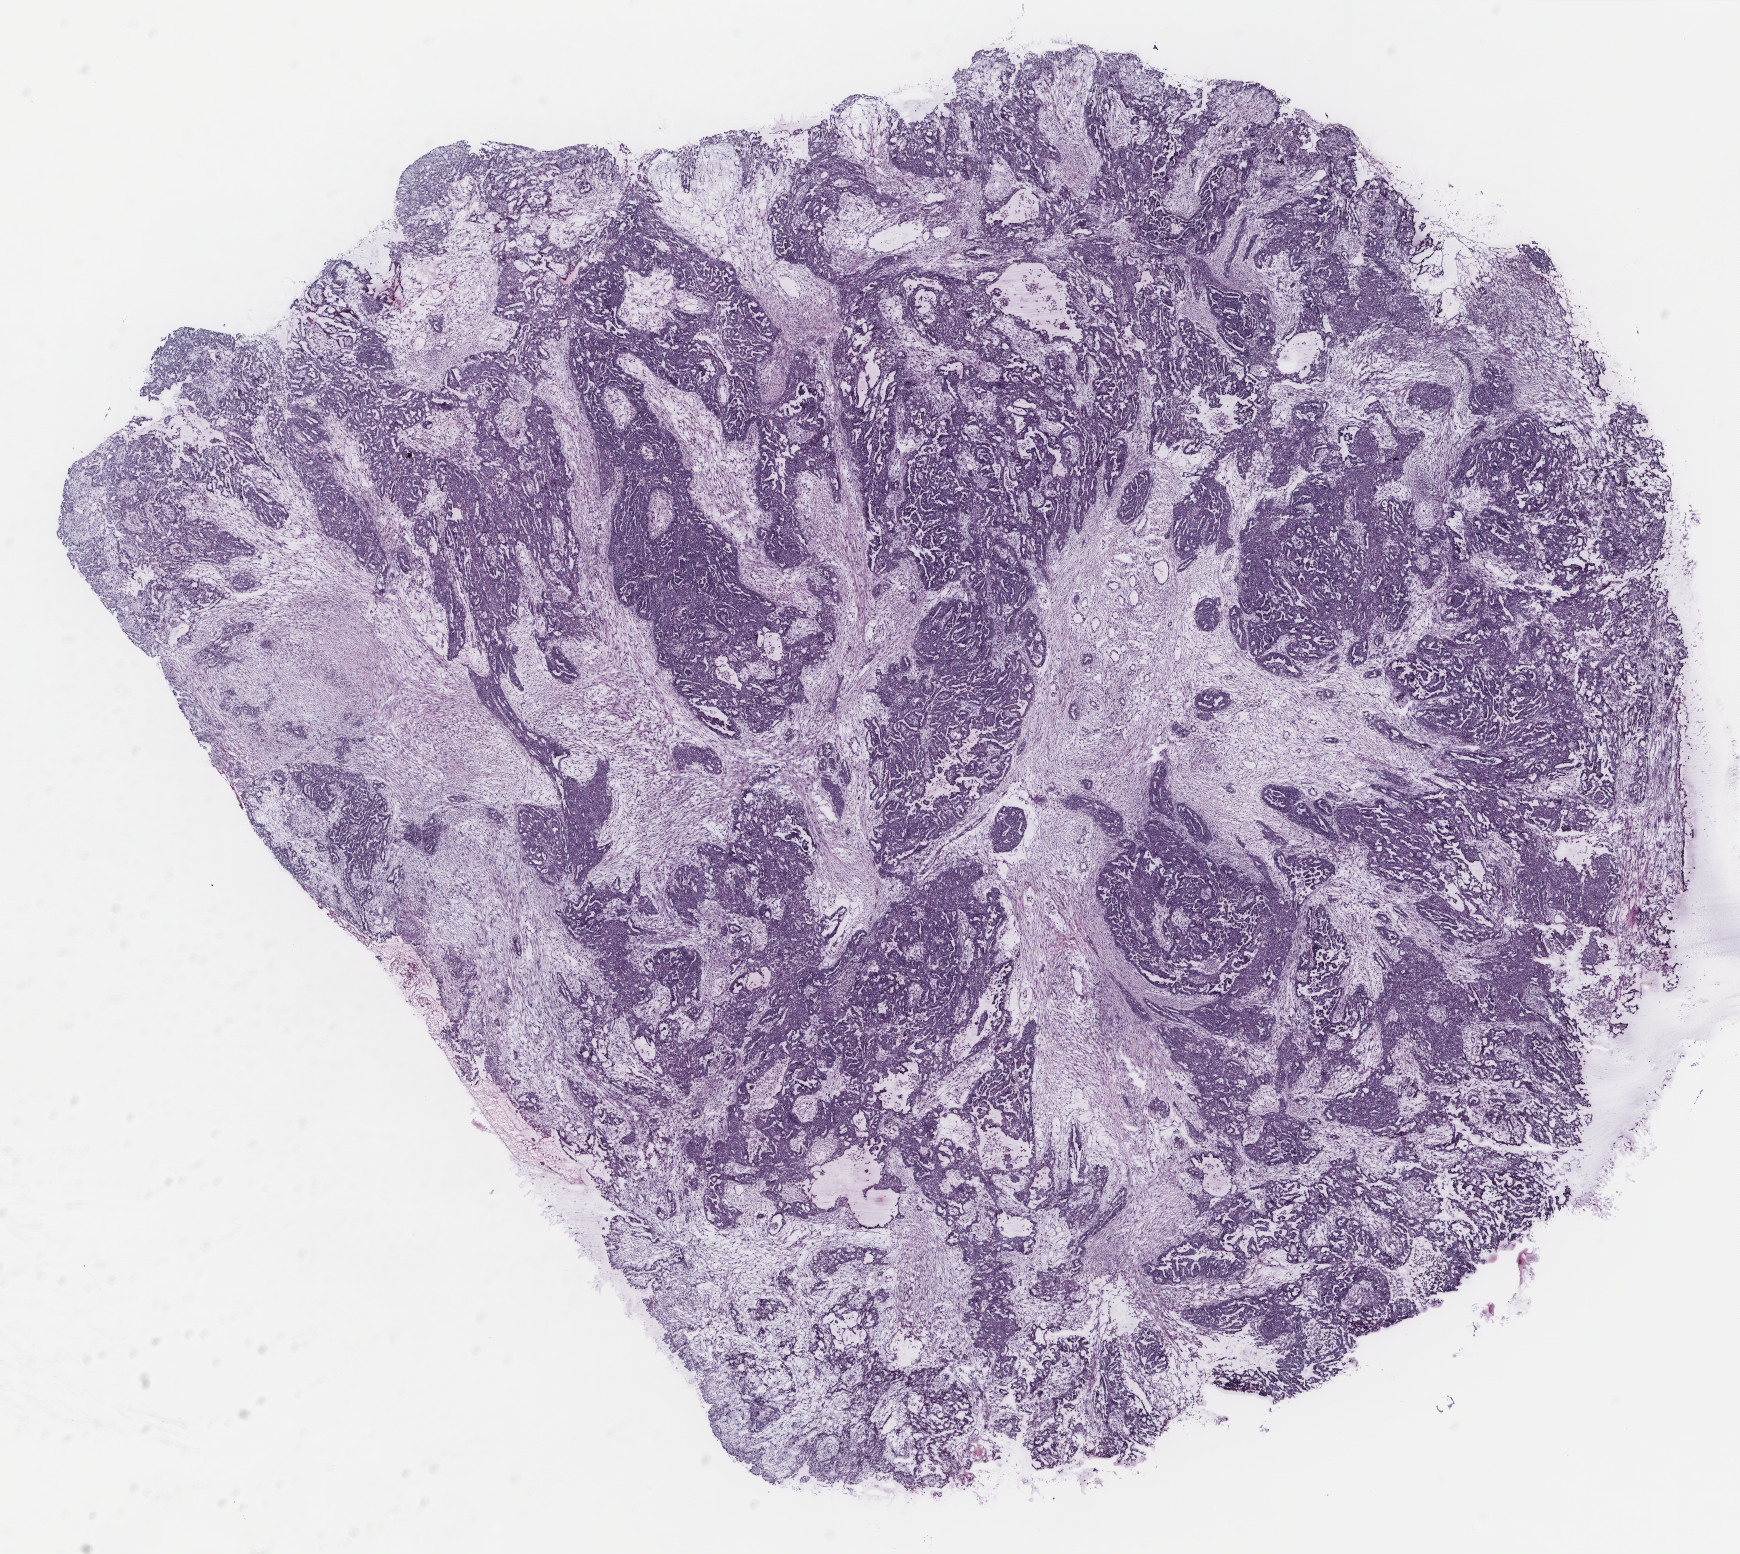
Digitized Hematoxylin and eosin (H&E) stained tissue section (whole slide), low-resolution overview of the scanned area, about 13.9 x 12.4 mm (acquisition: 40x scan); tumour tissue sample, ovary. 50-year-old female patient.
Primary tumour site (as recorded): ovary. Diagnosis: Serous adenocarcinoma, NOS.